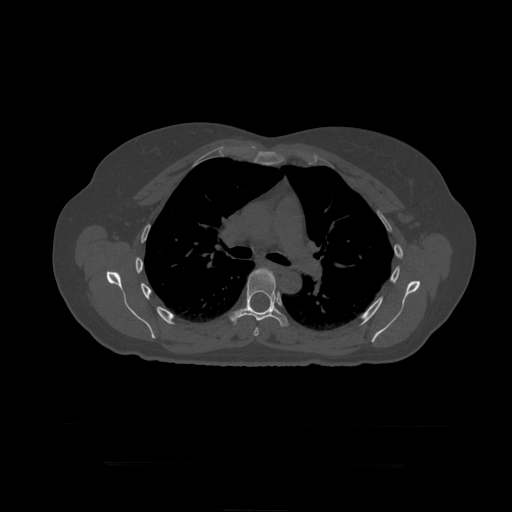
CT including the spine, one axial slice. Position 305 of 399 along the scan axis. Bone window (W 1800 / L 400 HU). 512 × 512 image matrix. Patient age 41 years. From the clinical record (not read from this slice): primary cancer: breast.
Structures marked on this image (semi-automatically segmented with operator editing):
- T6 vertebra: bounding box <254,327,259,336> (left, top, right, bottom; pixels)
- T7 vertebra: <230,268,289,327>